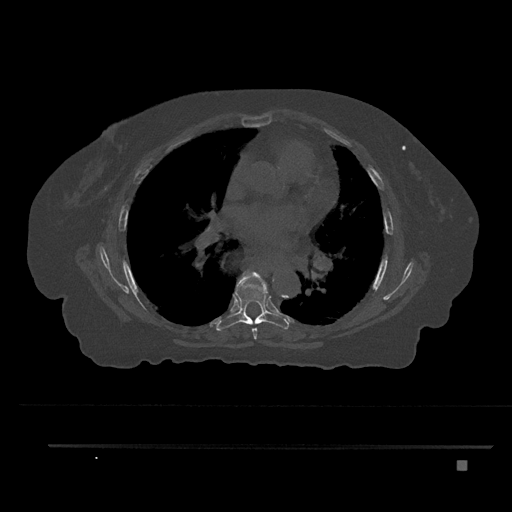
CT including the spine, one axial slice. Slice 497 of 797 in the series (ordered by position). Reconstruction kernel Br40s/3. Bone window (W 1800 / L 400 HU). 0.5 mm slice thickness. 512 × 512 image matrix, field of view 437 × 437 mm. Patient: female, 76 years. From the clinical record (not read from this slice): primary cancer: lung.
Structures marked on this image (semi-automatically segmented with operator editing):
- T6 vertebra: bounding box (x1, y1, x2, y2) in pixels: (244, 272, 267, 340)
- T7 vertebra: (216, 277, 290, 331)